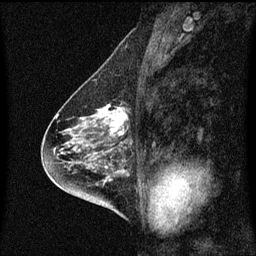
Breast MRI (dynamic contrast-enhanced), one sagittal slice; position 32 of 60 along the scan axis; dynamic contrast-enhanced series, image 2 of 3 at this slice position (ordered by acquisition); 1.5 T; TE 4.2 ms, TR 8.4 ms; 256 × 256 image matrix, field of view 200 × 200 mm. Patient: female, 58 years.
Structures marked on this image (semi-automatically segmented with operator editing):
- analysis volume of interest (the breast-tissue region the enhancement analysis was run in; not a lesion): bounding box [x1, y1, x2, y2] px = [86, 104, 132, 143]
- tumour enhancement mask (voxels above the 70 % enhancement threshold inside the analysis volume of interest): [91, 104, 128, 137]